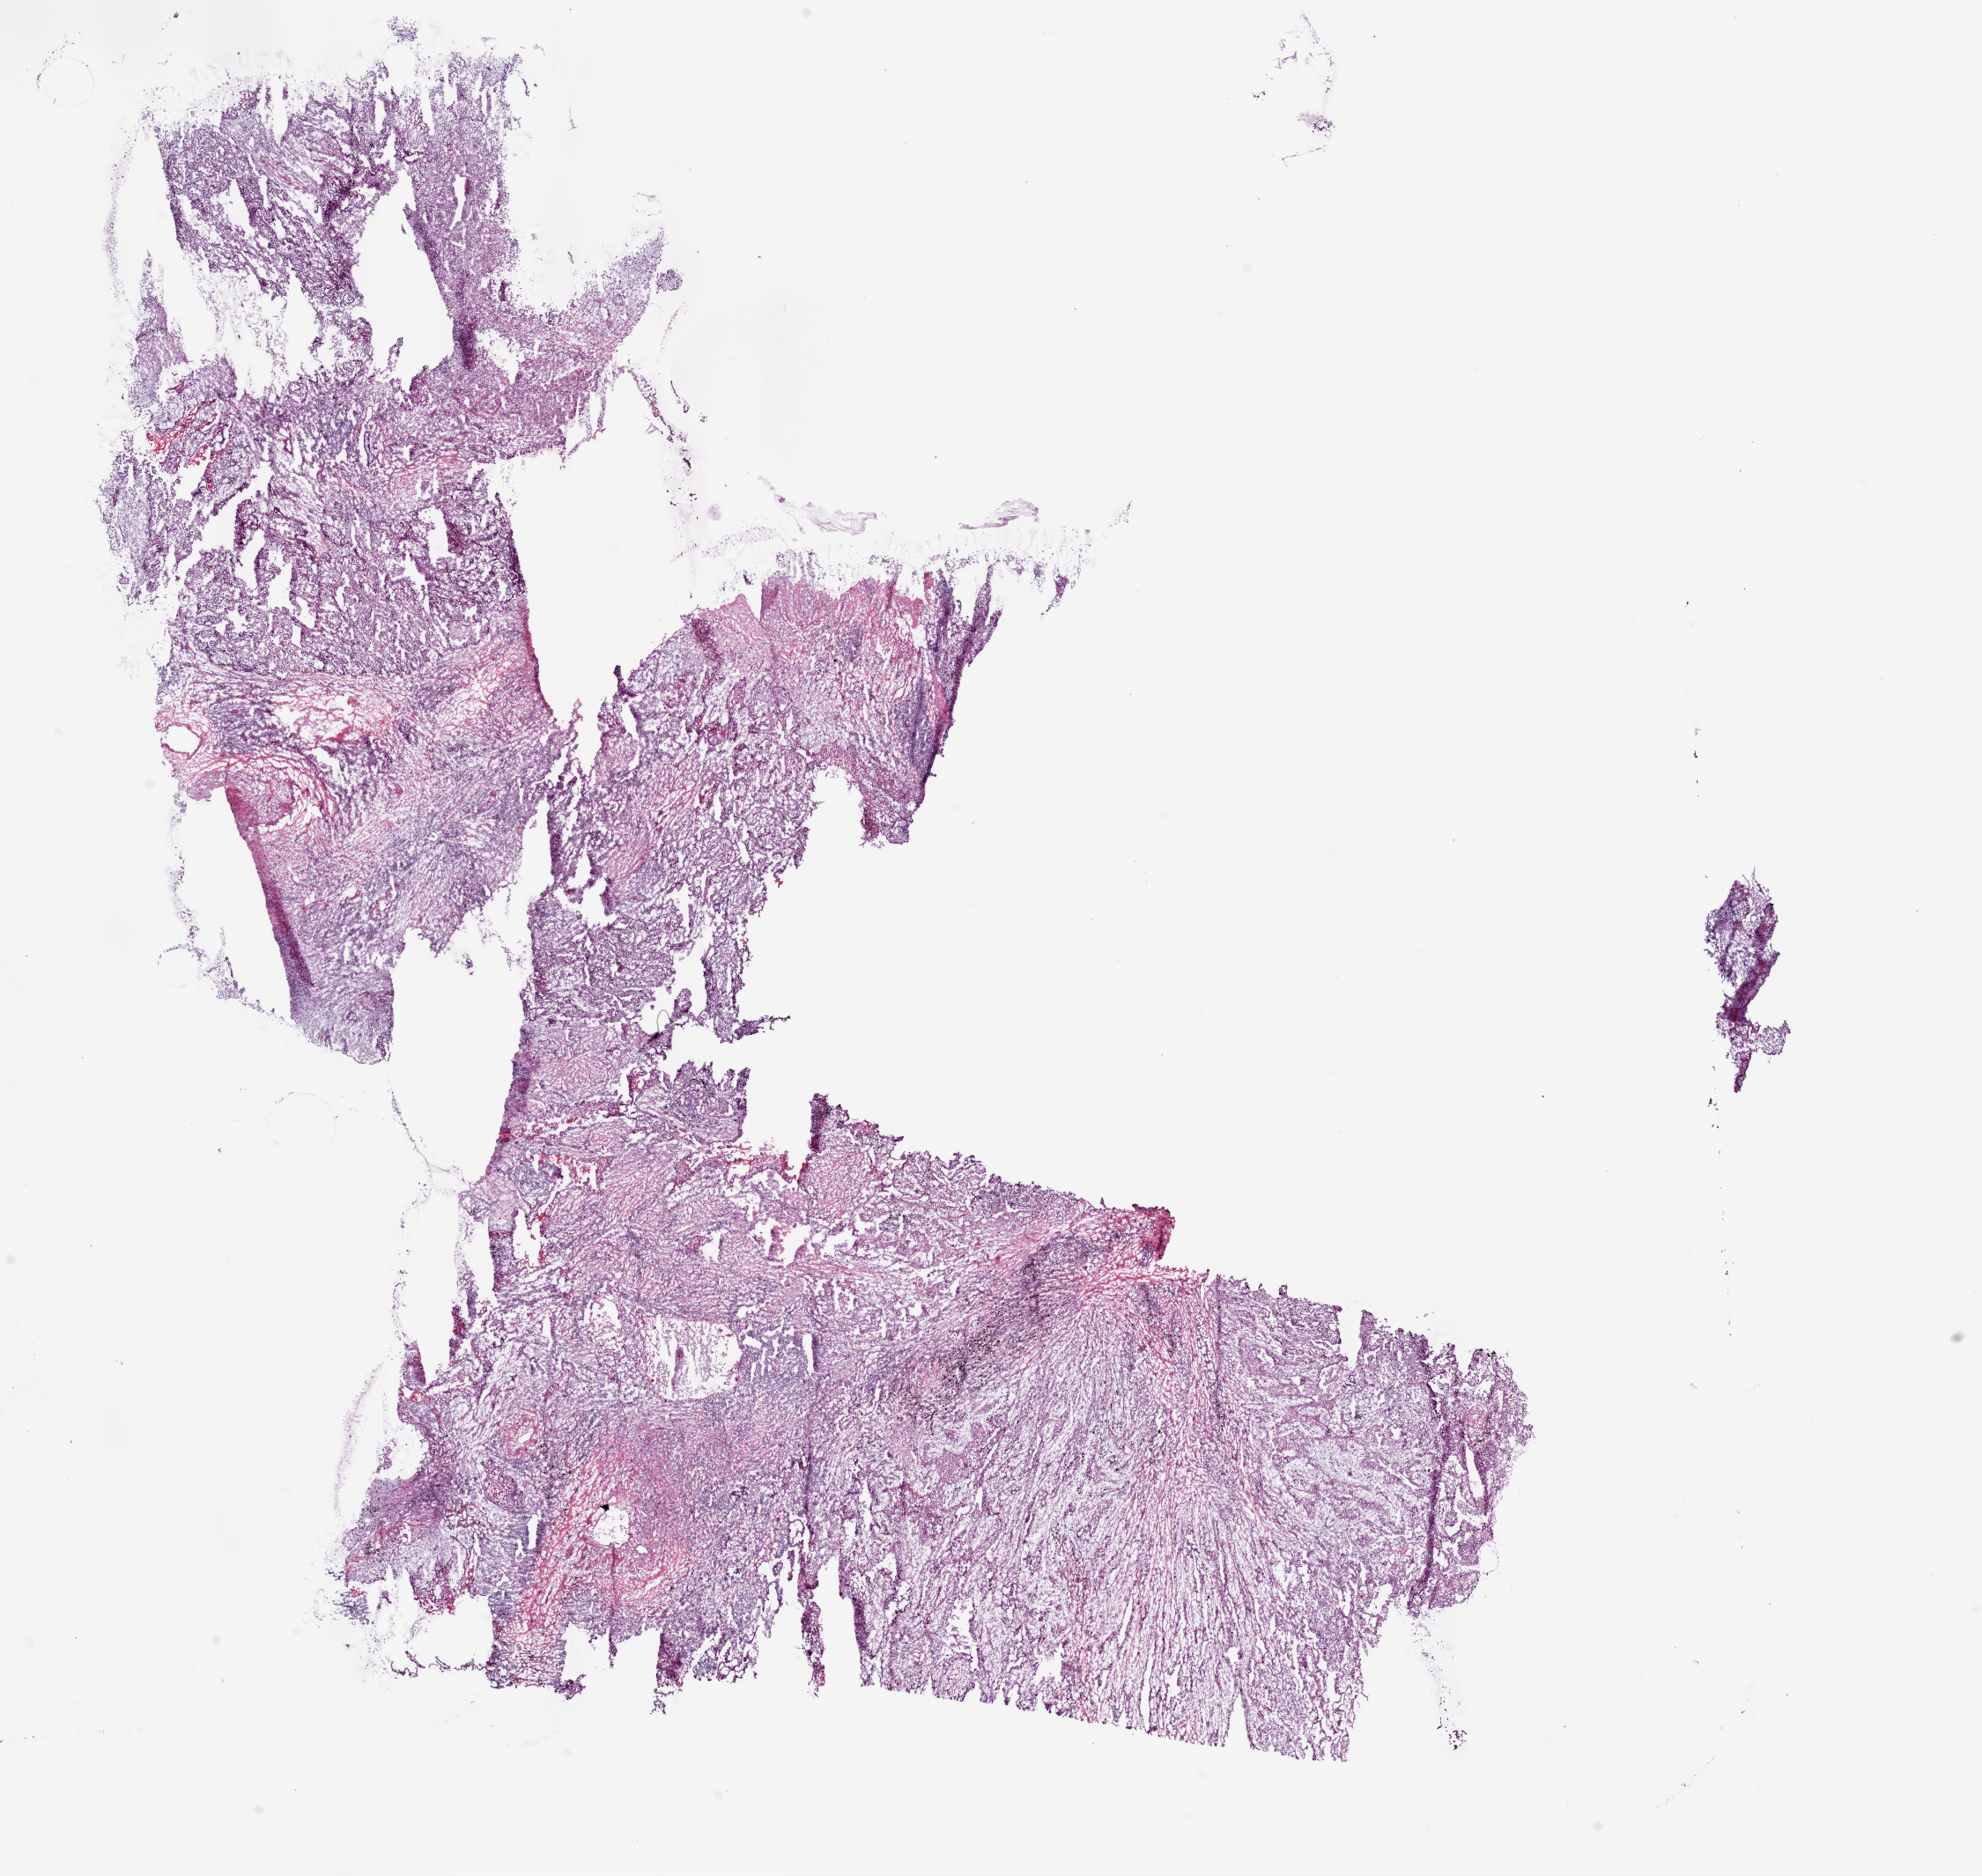
Hematoxylin and eosin (H&E) stained whole-slide image — shown as a low-resolution overview of the whole scanned area (about 18.1 x 17.1 mm, slide scanned at 20x), frozen section from the top of the tissue portion, sample: primary tumour, lung. Female patient; age at initial diagnosis 71 years. Slide review estimates, as recorded: tumour cells 80%, tumour nuclei 60%, normal cells 0%, stromal cells 20%, necrosis 0%.
- pathologic diagnosis: Squamous cell carcinoma, NOS
- AJCC pathologic stage: IA (6th edition)